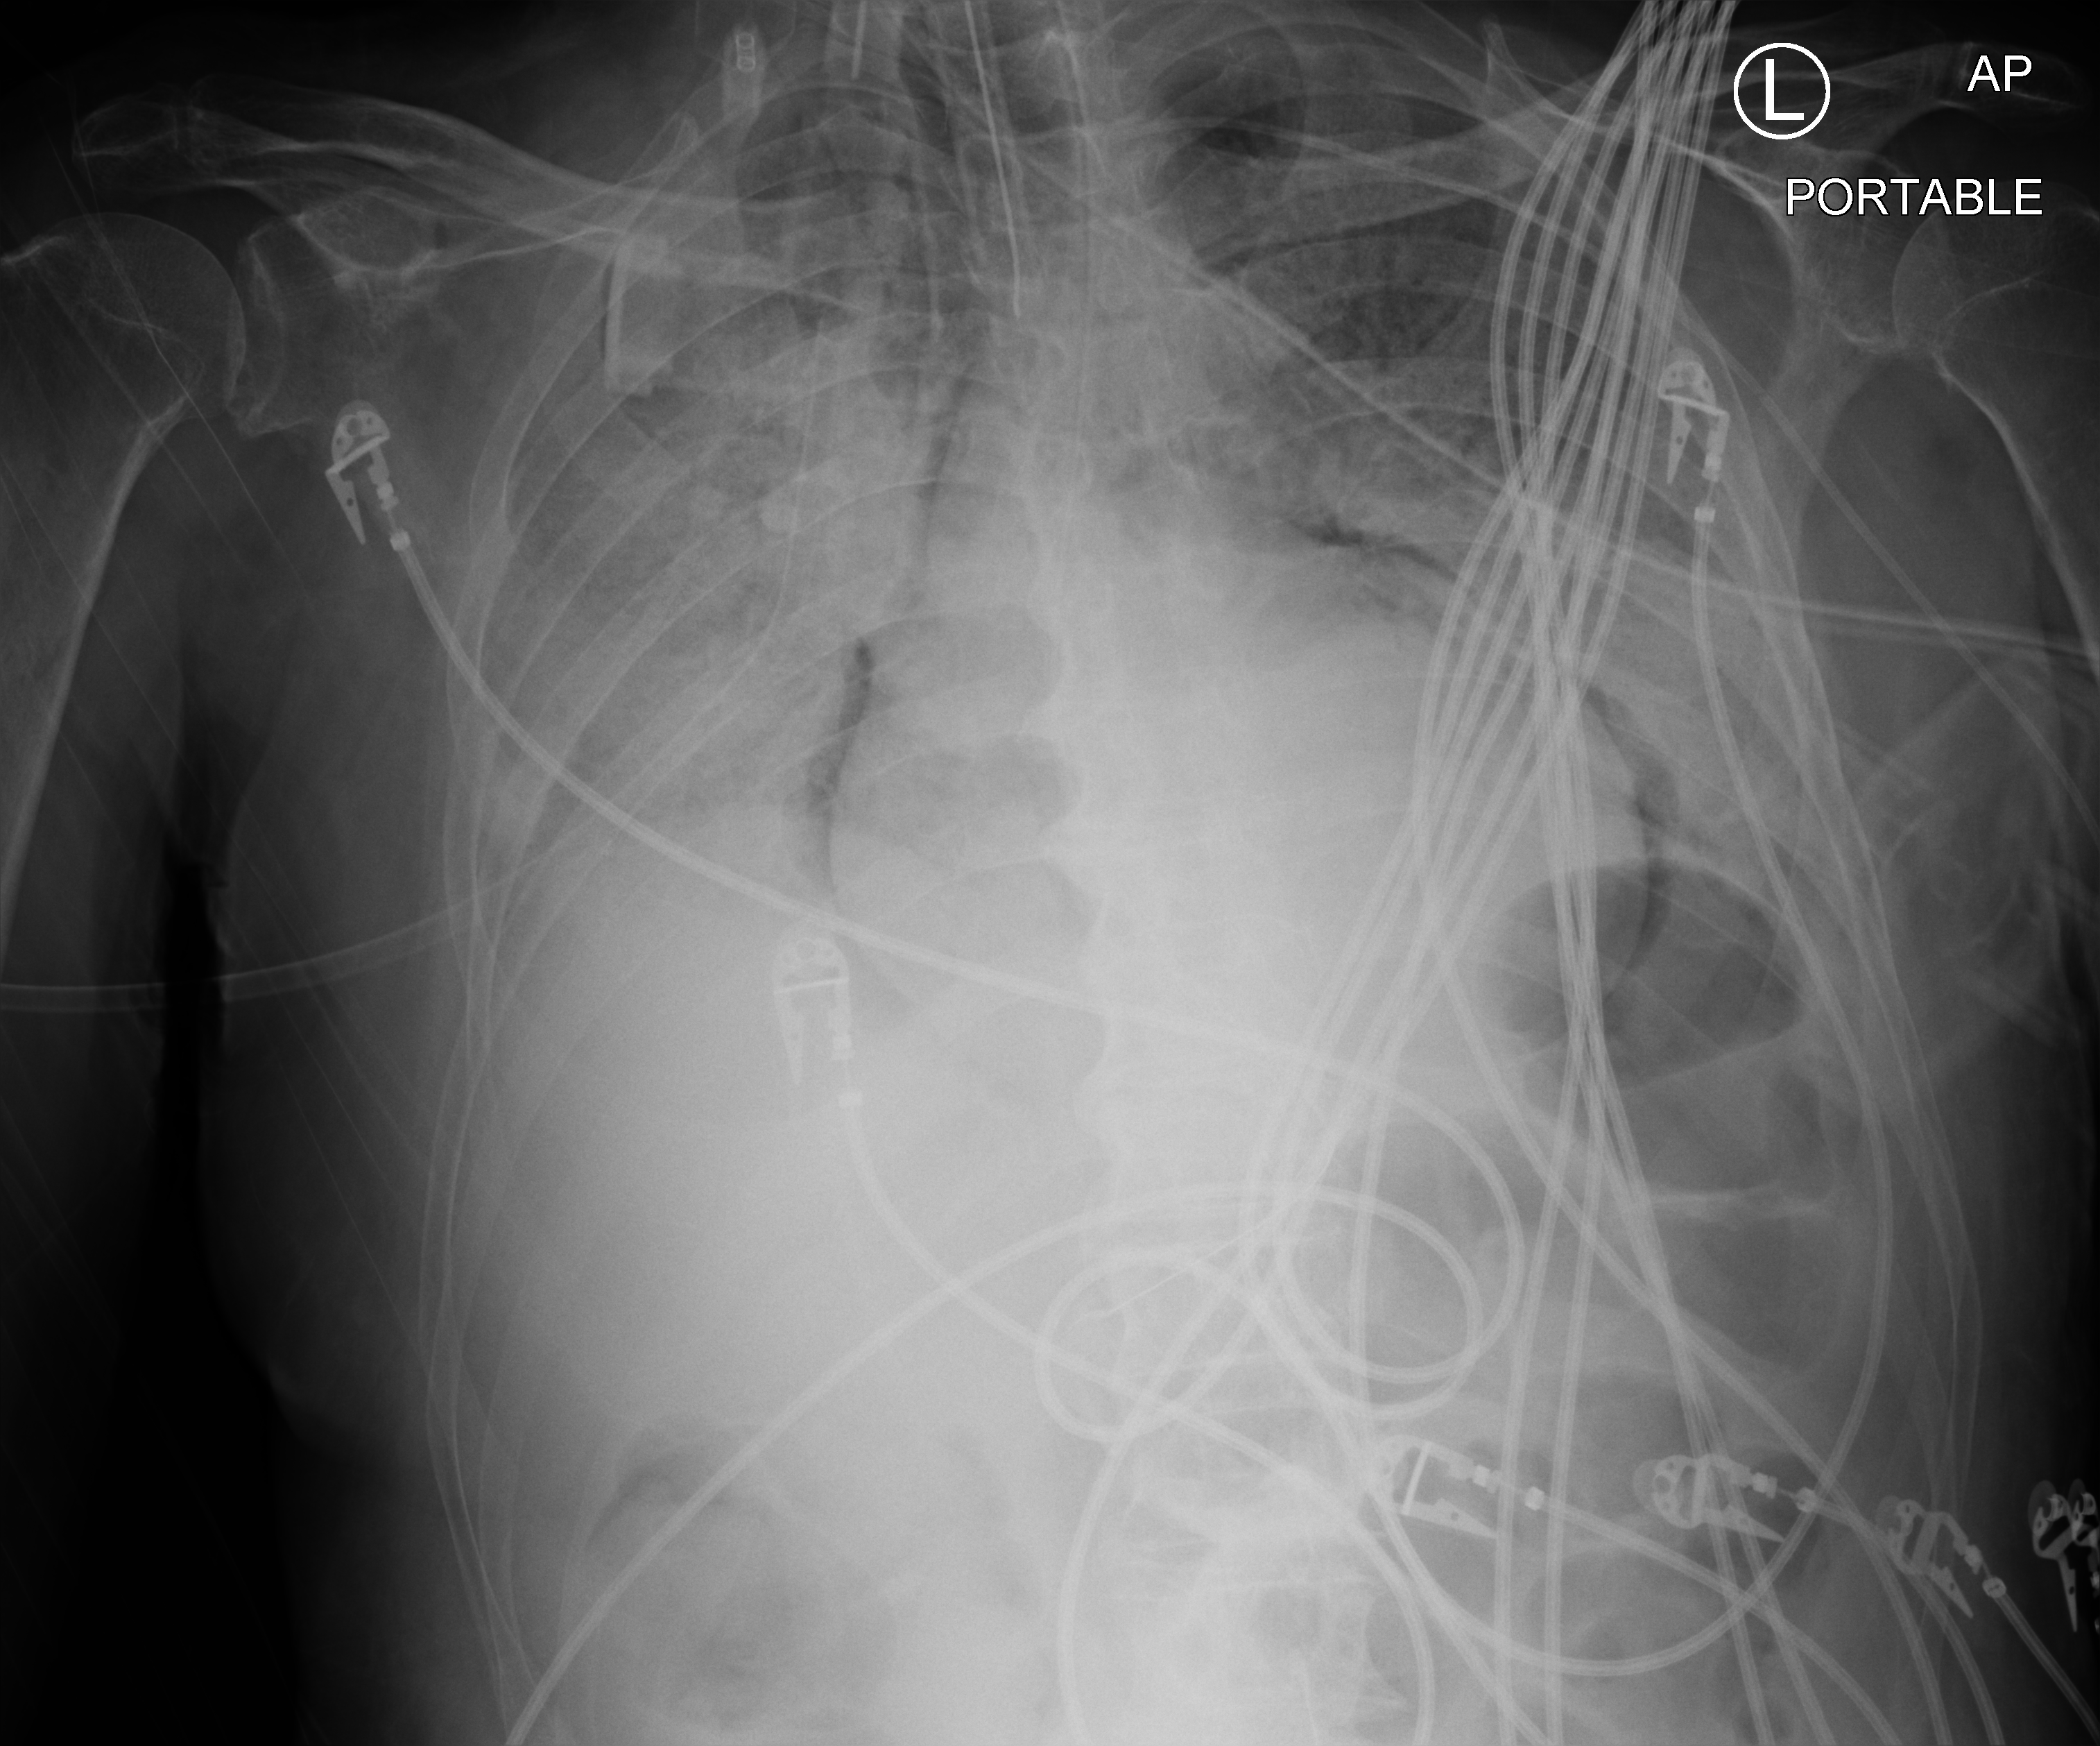
Bedside chest radiograph (computed radiography), anteroposterior (AP) projection. Patient hospitalised with COVID-19; male, aged 75–90 years.
From the hospital-stay record, not from the radiograph (when in the stay this image was taken is not recorded): mechanically ventilated during this hospital stay: yes.